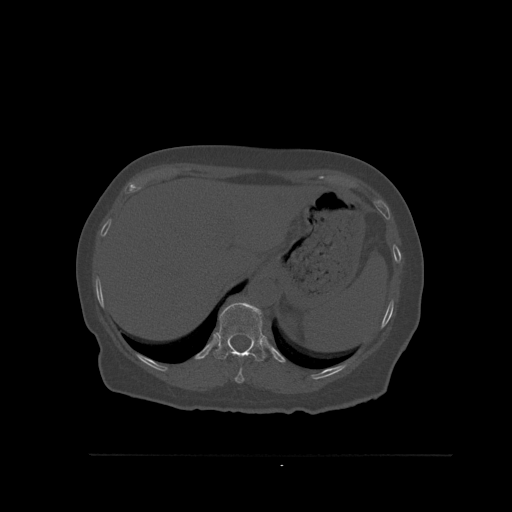
CT including the spine, one axial slice; slice 305 of 527 in the series (ordered by position); bone window (W 1800 / L 400 HU); 1.5 mm slice thickness; 512 × 512 image matrix. Patient: female, 73 years. Case-level facts recorded for this patient, not image findings: primary cancer: breast.
Annotated regions visible in this slice (semi-automatic segmentation, software-assisted and operator-edited):
- T10 vertebra: bounding box [x1, y1, x2, y2] px = [235, 367, 245, 383]
- T11 vertebra: [213, 302, 267, 361]